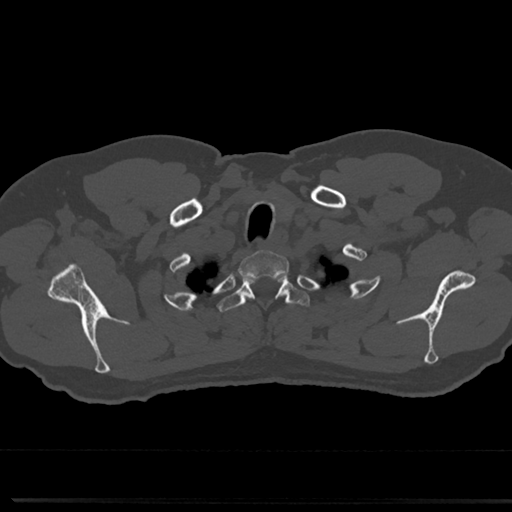
CT including the spine, one axial slice; slice 648 of 817 in the series (ordered by position); reconstruction kernel Br40s/3; 120 kVp; bone window (W 1800 / L 400 HU); 0.5 mm slice thickness; 512 × 512 image matrix, field of view 355 × 355 mm. Patient: male, 61 years. Case-level facts recorded for this patient, not image findings: primary cancer: prostate.
Outlined on this slice (semi-automatically segmented with operator editing):
- T1 vertebra: bounding box <242,251,287,267> (left, top, right, bottom; pixels)
- T2 vertebra: <225,273,305,325>